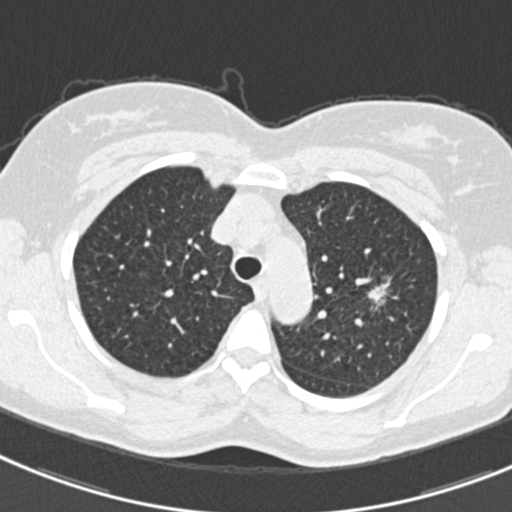
Low-dose screening chest CT, one axial slice; position 243 of 309 along the scan axis; lung window (W 1500 / L -600 HU); 1 mm slice thickness; 512 × 512 image matrix, field of view 302 × 302 mm.
Outlined on this slice (outlined manually by an expert reader):
- lesion 1 (tumor, upper lobe of left lung): bounding box <369,285,387,304> (left, top, right, bottom; pixels)